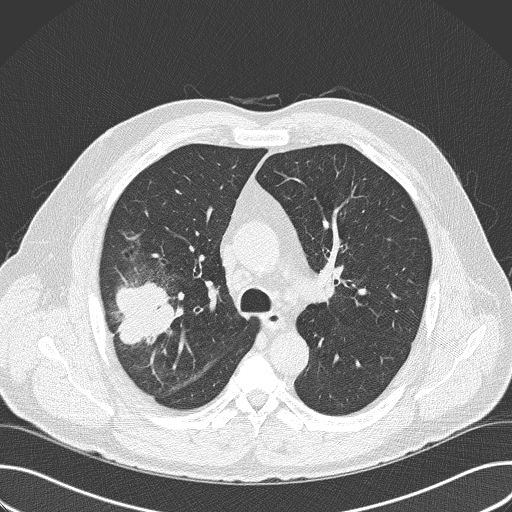
Low-dose screening chest CT, axial slice, first (baseline) screen, lung window (W 1500 / L -600 HU), 2 mm slice thickness, lung (sharp) reconstruction kernel (B50f). Male, age 56 years at enrolment.
- Expert-annotated lung lesion, bounding box [x1, y1, x2, y2] px = [82, 265, 187, 374].
- The exam's reader record, not a measurement of the box and not confirmed to be the same lesion: non-calcified nodule or mass ≥4 mm, right upper lobe, 6 × 5 mm, spiculated (stellate) margins, soft tissue attenuation.
- Lung cancer was diagnosed 16 days after this screen: adenocarcinoma, NOS, right upper lobe, poorly differentiated (G3), stage IIB (AJCC 6th edition), 60 mm at pathology.